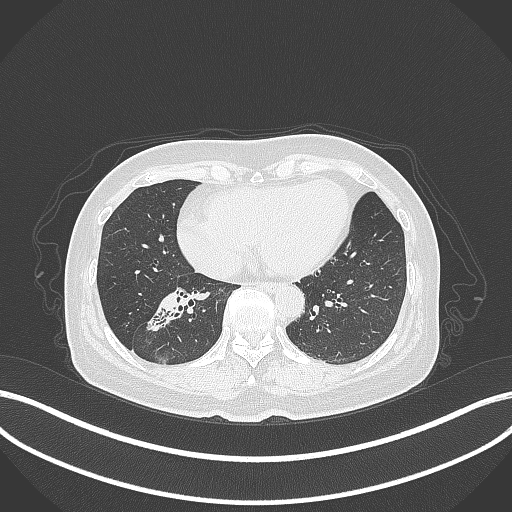
Chest CT, one axial slice; position 139 of 429 along the scan axis; reconstruction kernel B70f; 120 kVp; lung window (W 1500 / L -600 HU); 1 mm slice thickness; 512 × 512 image matrix, field of view 400 × 400 mm. Female patient, age 67 years. Case-level facts recorded for this patient, not image findings: clinical TNM (as recorded): T1c N1 M0.
Outlined on this slice (rectangle marked by the reading radiologist):
- lung tumour (recorded histology: adenocarcinoma): bounding box [x1, y1, x2, y2] px = [147, 290, 194, 332]